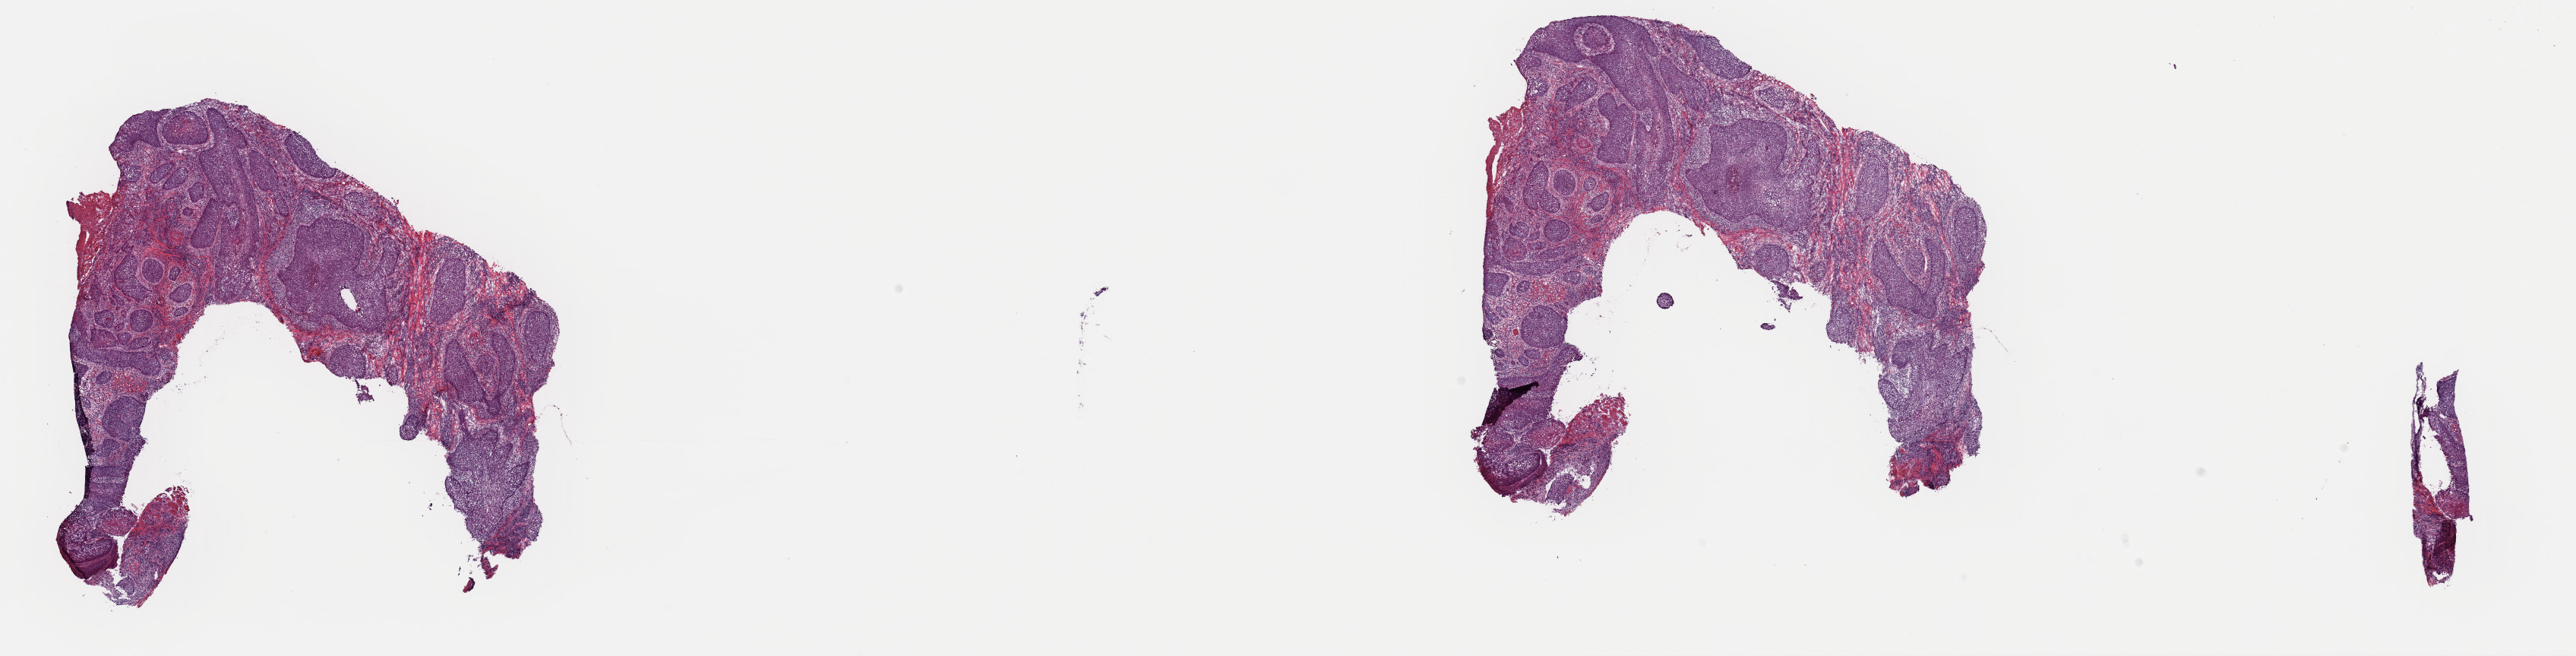
Hematoxylin and eosin (H&E) stained whole-slide image — a low-resolution overview of the entire scanned area, about 26.8 x 6.8 mm; frozen section; head and neck, primary tumour sample. Female, age 79 years at initial diagnosis. Histologic grade: G2 (moderately differentiated). Pathologist review of this section (percent, as recorded): tumour cells 70%, tumour nuclei 70%, normal cells 5%, stromal cells 24%, necrosis 1%. Inflammatory infiltration, as recorded: lymphocyte infiltration 30%, monocyte infiltration 0%, neutrophil infiltration 0%.
• laterality: right
• TNM: T2 N1 MX
• diagnosis: Squamous cell carcinoma, NOS
• AJCC pathologic stage: III (7th edition)